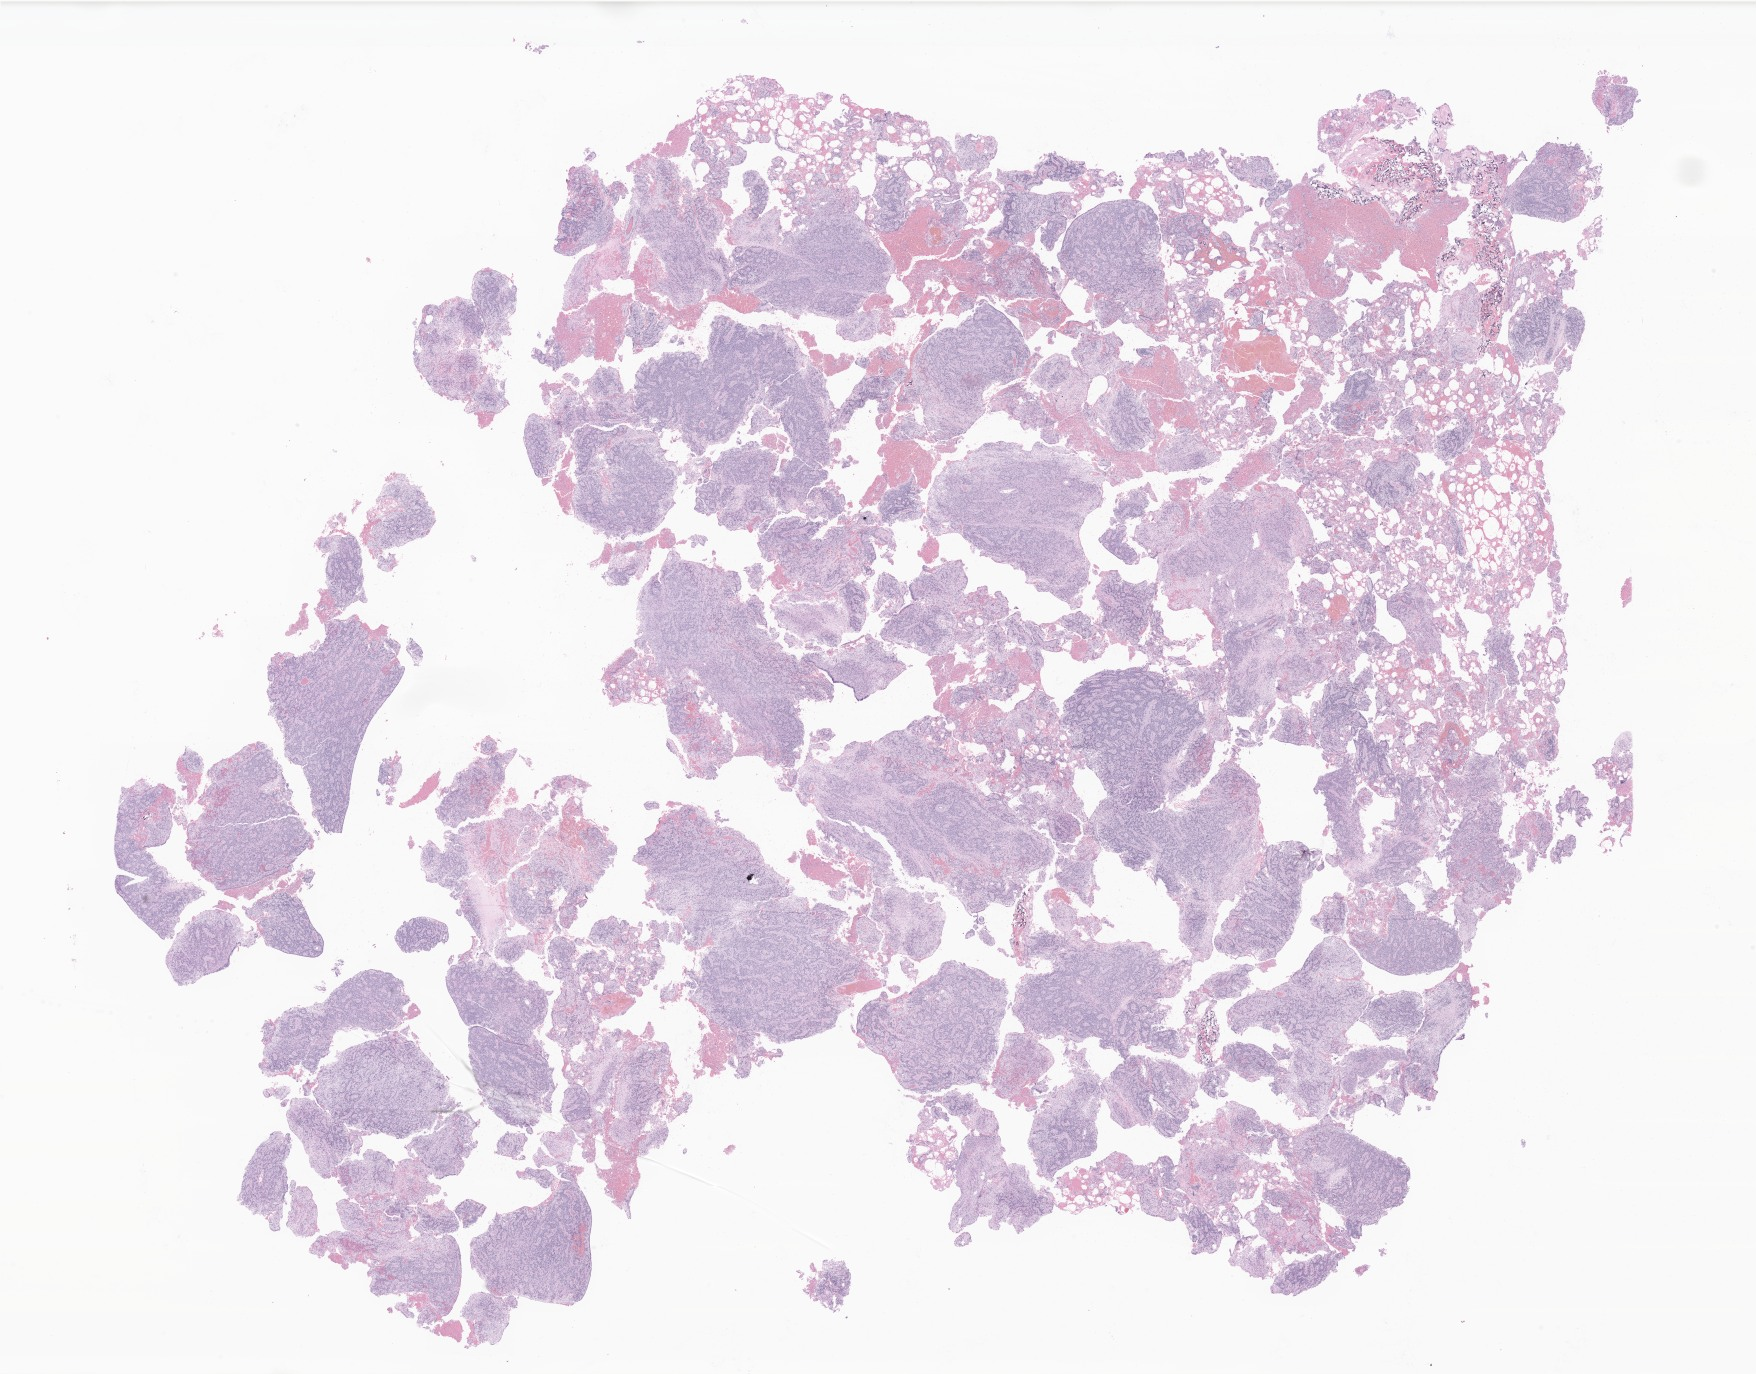
H&E whole-slide image of tumor tissue from the brain, shown as a low-resolution overview of the whole scanned area (about 29.6 x 23.2 mm); formalin-fixed paraffin-embedded section. Patient: male, age 434 days (about 1.2 years).
Recorded diagnosis: Ependymoma, NOS.